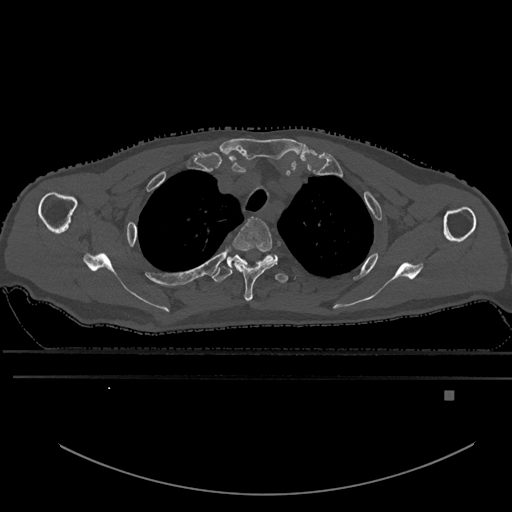
CT including the spine, one axial slice. Slice 480 of 969 in the series (ordered by position). Bone window (W 1800 / L 400 HU). 0.5 mm slice thickness. 512 × 512 image matrix, field of view 456 × 456 mm. Male patient, age 82 years. Case-level facts recorded for this patient, not image findings: primary cancer: prostate.
Annotated regions visible in this slice (semi-automatic segmentation, software-assisted and operator-edited):
- T2 vertebra: bounding box <227,217,278,302> (left, top, right, bottom; pixels)
- T3 vertebra: <211,254,288,284>